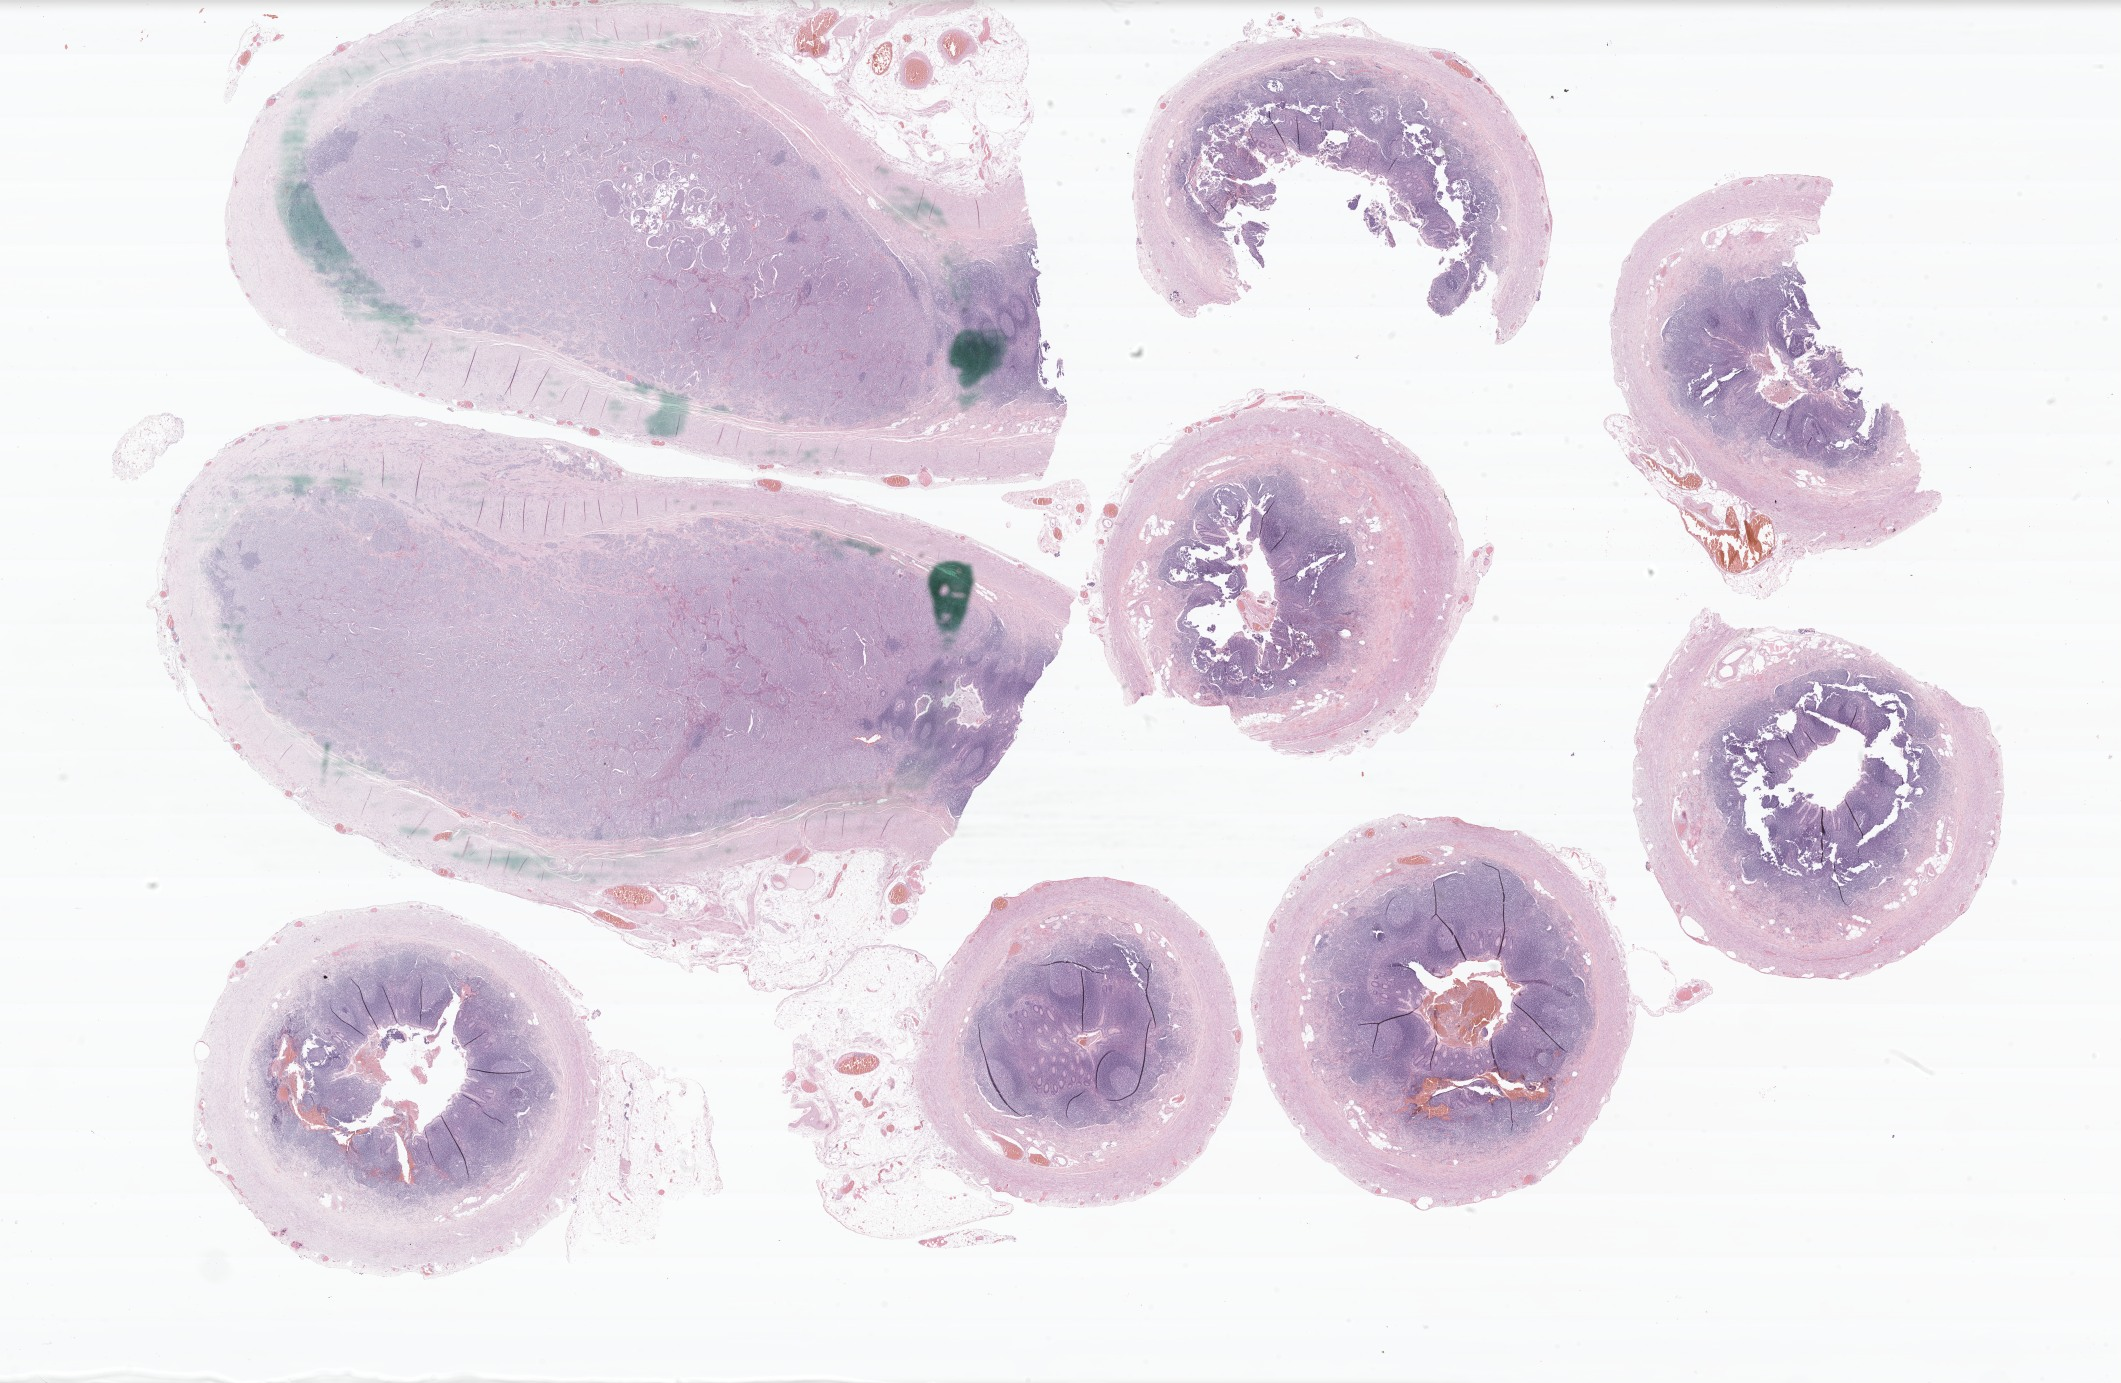
Whole-slide image, haematoxylin and eosin stain of tumor tissue from the appendix — a low-resolution overview of the entire scanned area, about 35.7 x 23.3 mm, formalin-fixed paraffin-embedded section. Patient male; age 203 months (16 years 11 months).
Diagnosis (ICD-O-3 morphology term): Neuroendocrine carcinoma, NOS.